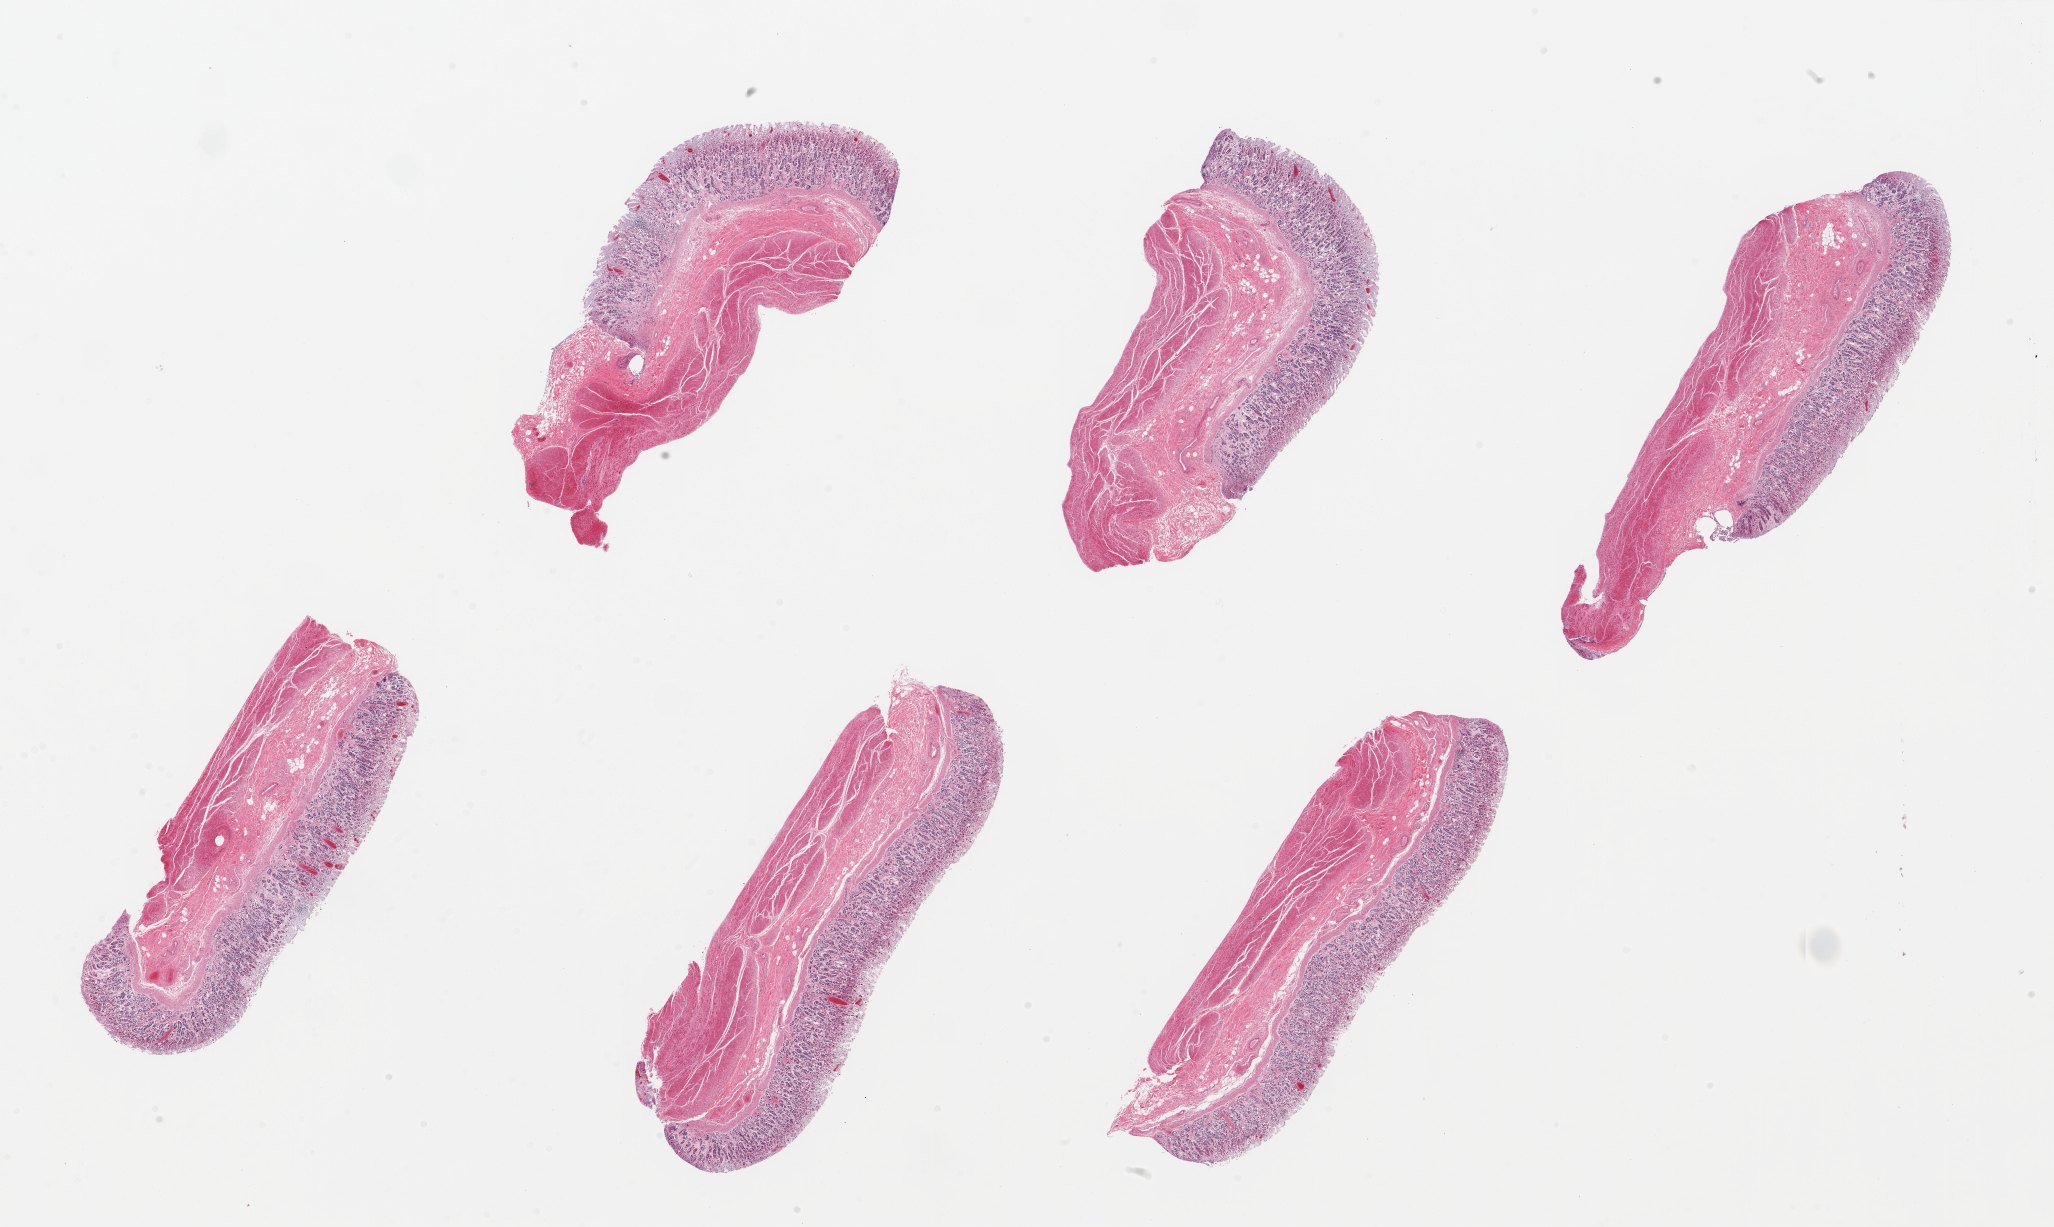
Hematoxylin and eosin (H&E) whole-slide image, brightfield, low-resolution overview of the scanned area, about 32.5 x 19.4 mm (acquisition: 20x scan). PAXgene-fixed, paraffin-embedded tissue. Section of stomach (target tissue). Donor tissue sample. Female donor.
Pathologist's review note for this sample: 6 pieces. up to 8x3mm; mucosa=3;muscle=2 (autolysis).